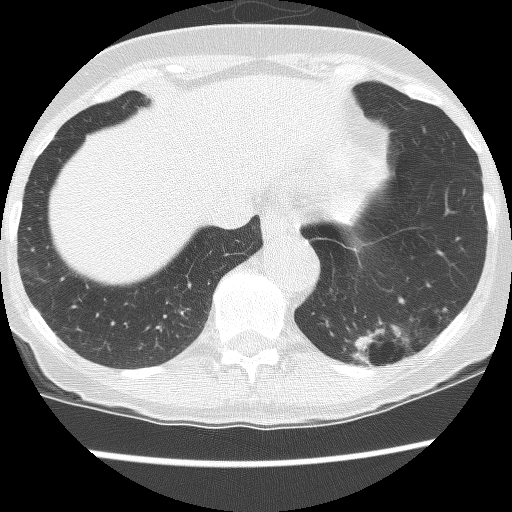
Low-dose screening chest CT, axial slice; third screening round (two years after baseline); lung window (W 1500 / L -600 HU); 120 kVp; slice 101 of 130 in the series; 512 × 512 image matrix, field of view 290 × 290 mm. Female participant, aged 61 years at enrolment. Current smoker at enrolment.
• Expert-annotated lung lesion, bounding box [x1, y1, x2, y2] px = [335, 294, 441, 385].
• The screening reader recorded 2 non-calcified nodules or masses ≥4 mm on this exam (left lower lobe, left lower lobe); which of them this box marks is not recorded.
• Official screen result: positive, no significant change: stable abnormalities potentially related to lung cancer, unchanged since the prior screening exam.
• Later outcome: lung cancer diagnosed 166 days after this screen — non-small cell carcinoma, left lower lobe, poorly differentiated (G3), stage IB (AJCC 6th edition), 100 mm at pathology.